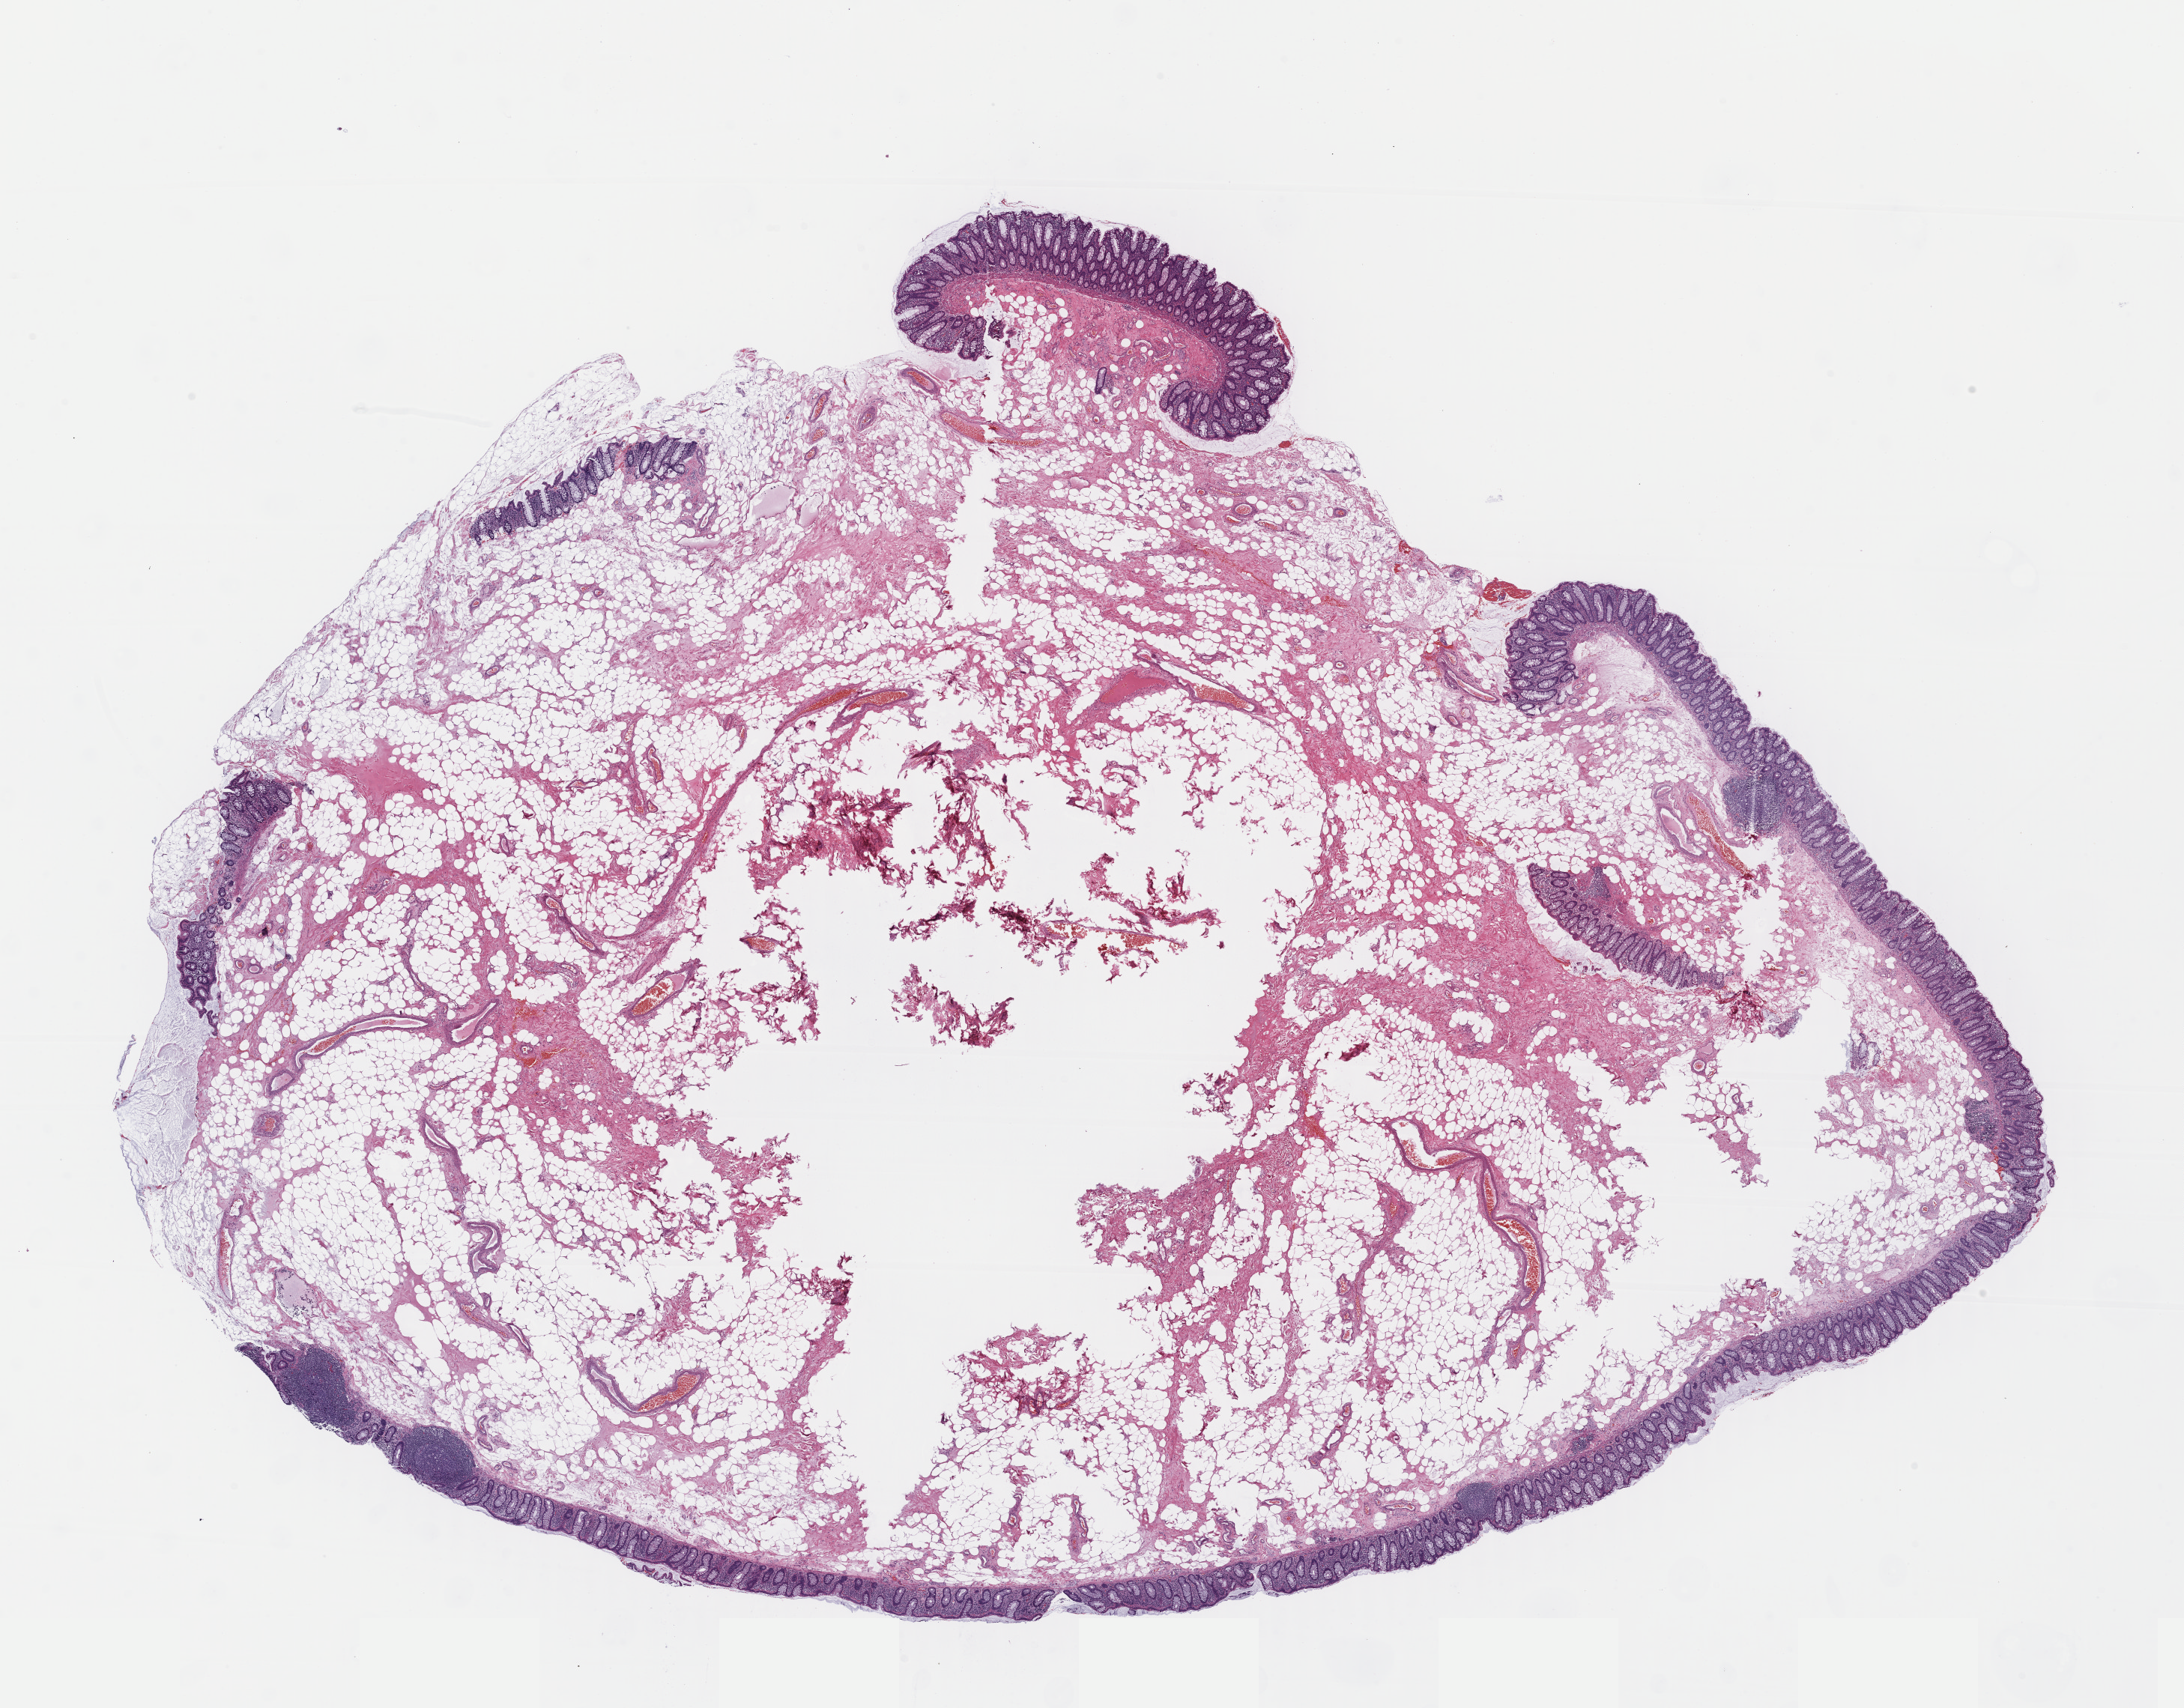
H&E-stained whole-slide image — low-resolution overview of the scanned area, about 23.0 x 18.0 mm; formalin-fixed paraffin-embedded (FFPE) diagnostic section; colon, primary tumour sample. Male patient; age at initial diagnosis 59 years.
Lymph nodes positive (case pathology): 1 of 60 examined. AJCC pathologic stage: IIIB (7th edition). TNM: T3 N1 M0. Pathologic diagnosis: Adenocarcinoma, NOS (transverse colon).